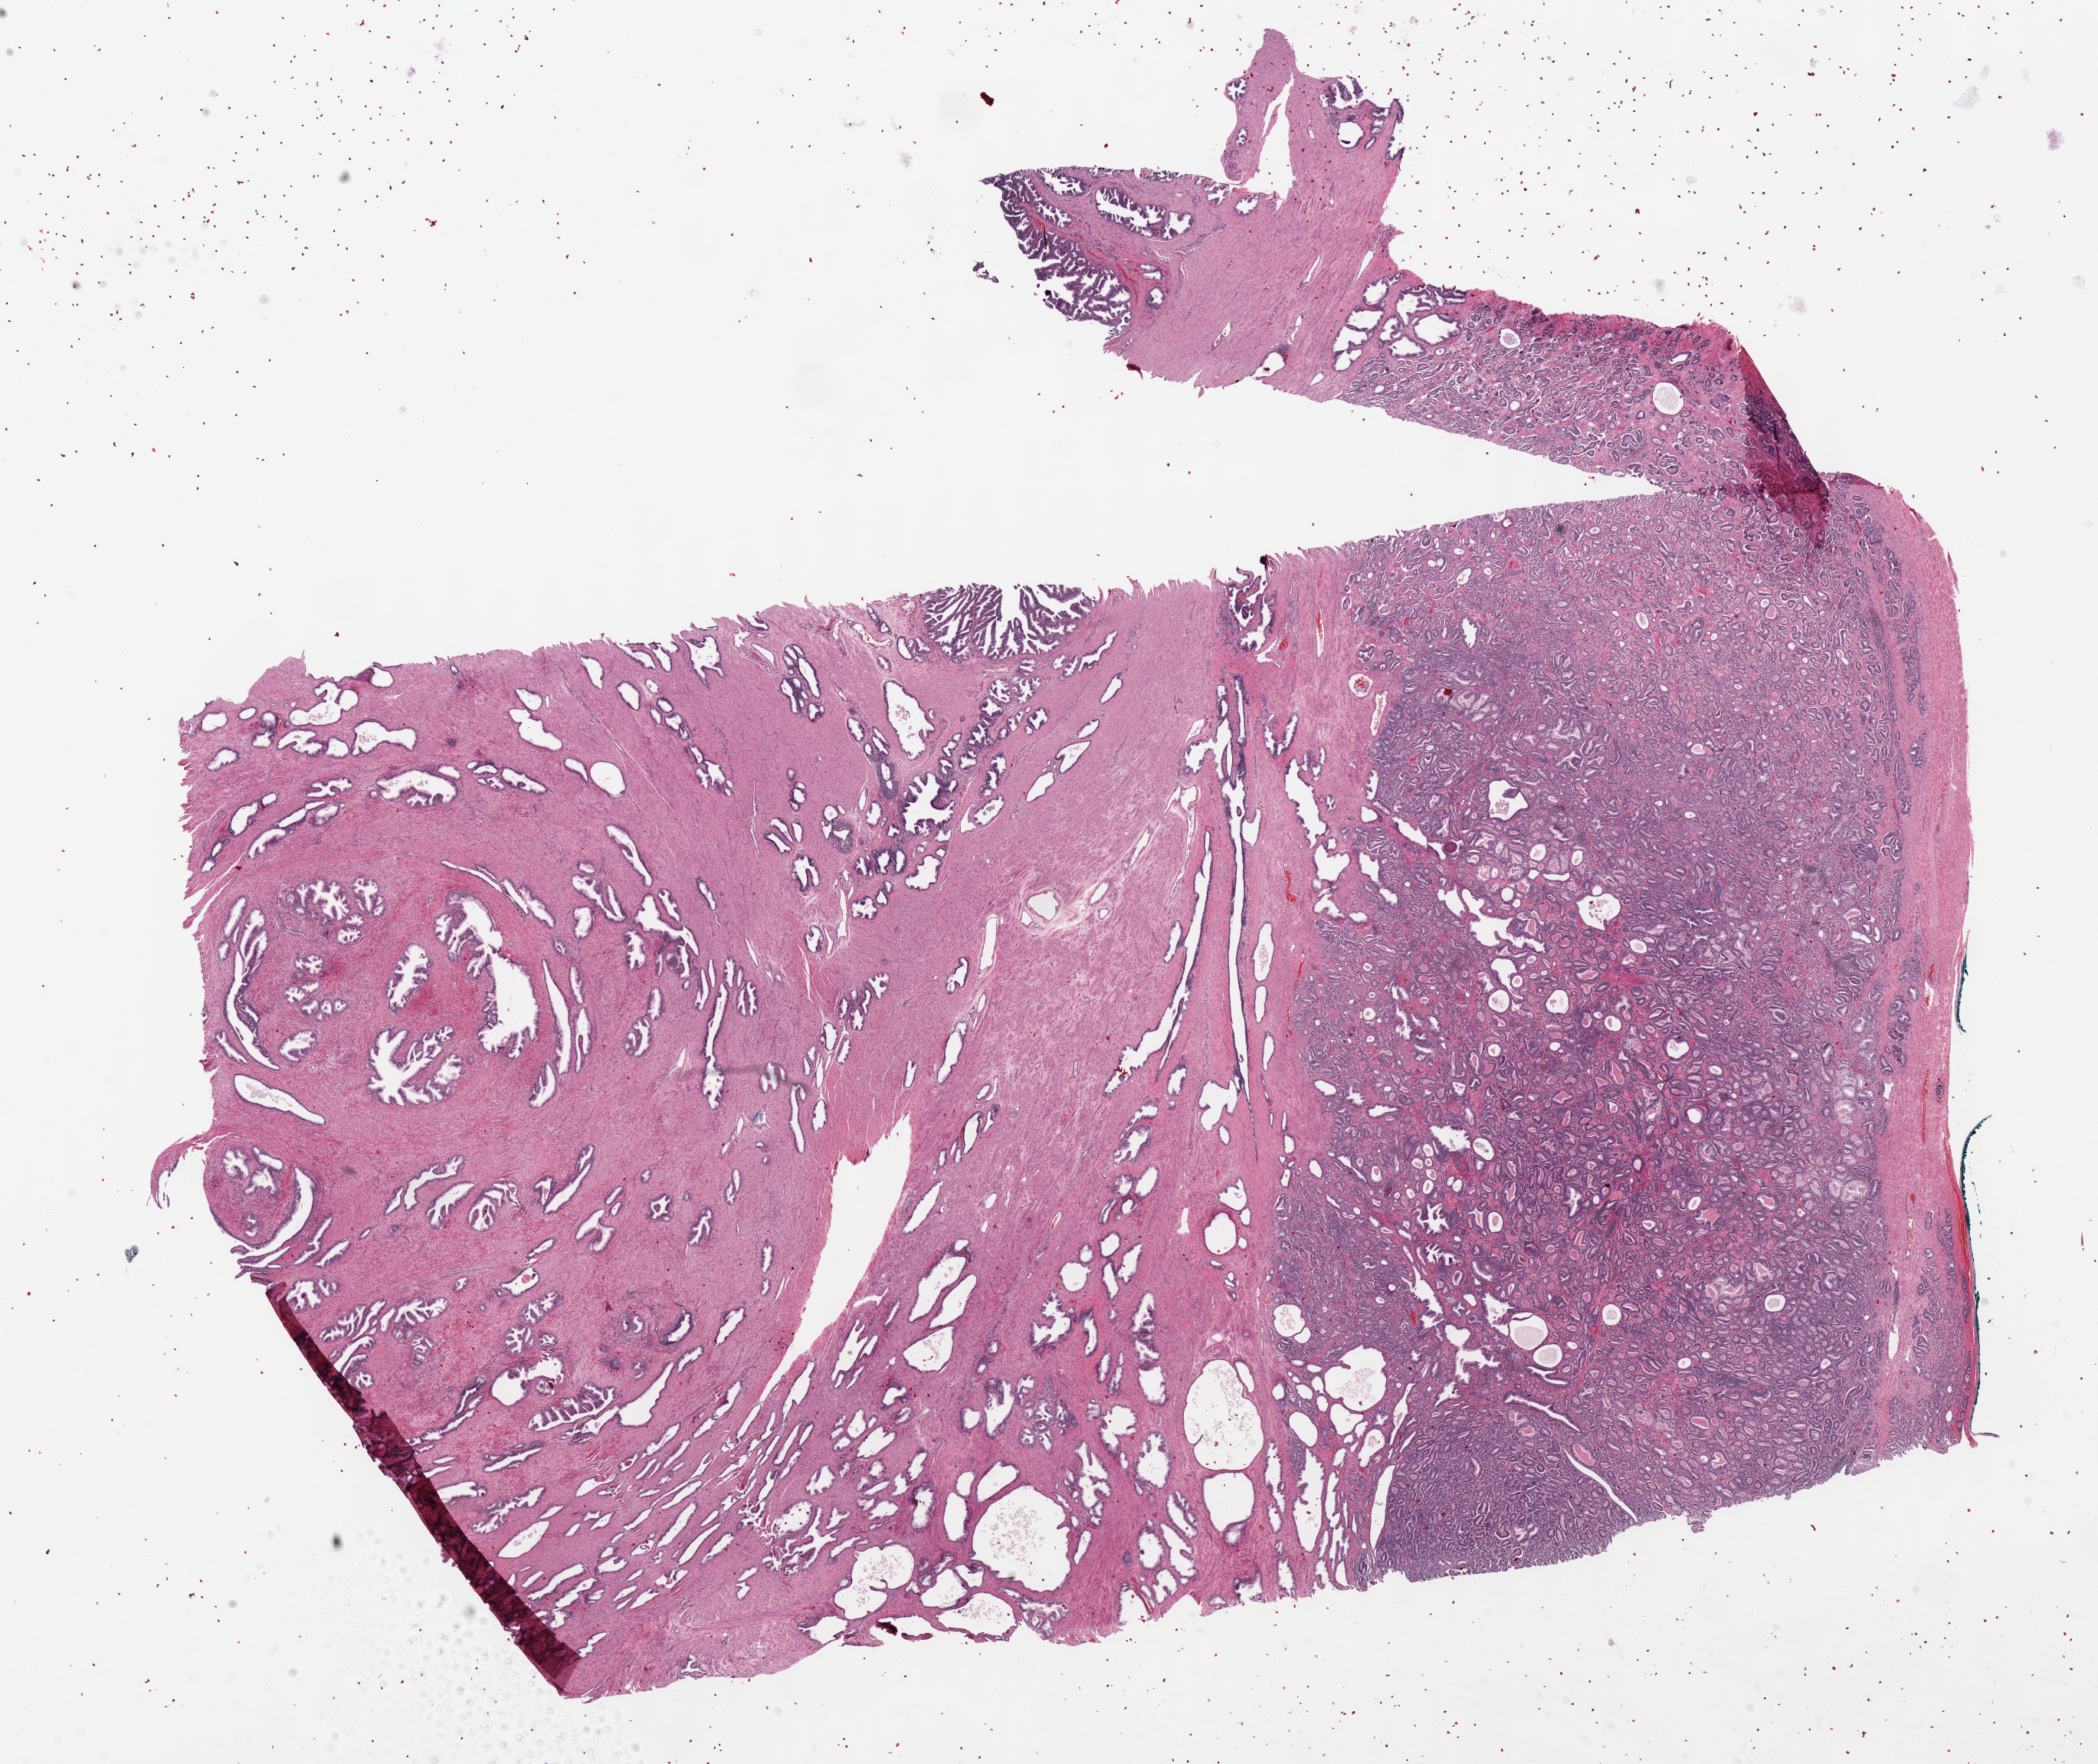
Digitized H&E tissue section (whole slide), shown as a low-resolution overview of the whole scanned area (about 22.1 x 18.6 mm, acquisition: 40x scan), formalin-fixed paraffin-embedded (FFPE) diagnostic section, sample: primary tumour, prostate. Patient: male, age at initial diagnosis 52 years. Gleason score: 6 (3+3).
Laterality: right. Histologic diagnosis: Adenocarcinoma, NOS (prostate gland). Lymph nodes positive (case pathology): 0 of 16 examined.